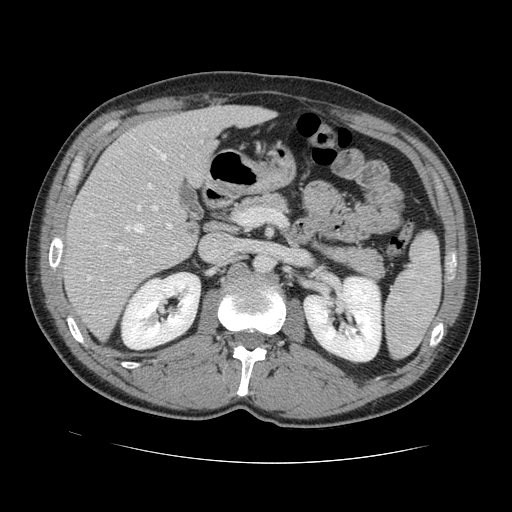
Contrast-enhanced abdominal CT, one axial slice; slice 71 of 131 in the series (ordered by position); 120 kVp; intravenous contrast given; soft-tissue window (W 400 / L 40 HU); 512 × 512 image matrix, field of view 380 × 380 mm. Male patient, age 40 years. From the clinical record (not read from this slice): diagnosis: colorectal cancer liver metastases, imaged before liver resection; multiple liver metastases: yes; largest metastasis: 2.9 cm; disease in both lobes: yes.
Annotated regions visible in this slice (expert manual segmentation):
- hepatic veins: box from (x=87, y=145) to (x=167, y=281) px
- liver: (x=66, y=107)–(x=269, y=338)
- planned liver remnant (the part of the liver to remain after resection): (x=108, y=106)–(x=268, y=191)
- portal vein (with intrahepatic branches): (x=127, y=183)–(x=172, y=264)
- liver metastasis: (x=189, y=227)–(x=195, y=234)